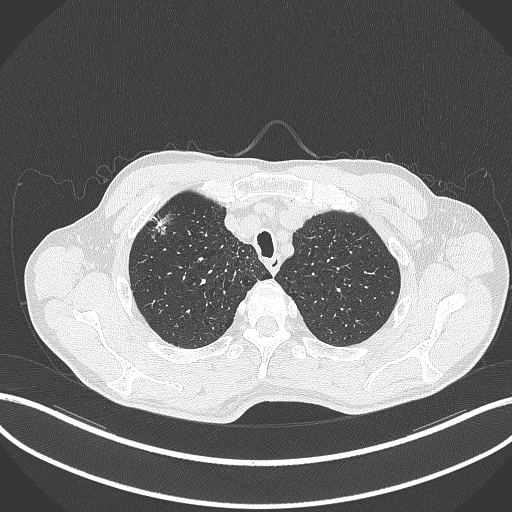
Chest CT, one axial slice. Position 359 of 427 along the scan axis. Reconstruction kernel B70f. 120 kVp. Lung window (W 1500 / L -600 HU). 1 mm slice thickness. 512 × 512 image matrix, field of view 400 × 400 mm. Patient: male, 69 years. From the clinical record (not read from this slice): clinical TNM (as recorded): T1b N1 M0.
Annotated regions visible in this slice (rectangle marked by the reading radiologist):
- lung tumour (recorded histology: adenocarcinoma): bounding box (x1, y1, x2, y2) in pixels: (146, 211, 175, 236)